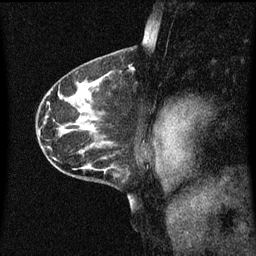
Breast MRI (dynamic contrast-enhanced), one sagittal slice. Position 38 of 60 along the scan axis. Dynamic contrast-enhanced series, image 2 of 3 at this slice position (ordered by acquisition). 1.5 T. TE 4.2 ms, TR 8.4 ms. 2 mm slice thickness. 256 × 256 image matrix, field of view 200 × 200 mm. Female patient, age 41 years.
Annotated regions visible in this slice (semi-automatically segmented with operator editing):
- analysis volume of interest (the breast-tissue region the enhancement analysis was run in; not a lesion): box from (x=121, y=58) to (x=137, y=83) px
- tumour enhancement mask (voxels above the 70 % enhancement threshold inside the analysis volume of interest): (x=129, y=66)–(x=136, y=71)